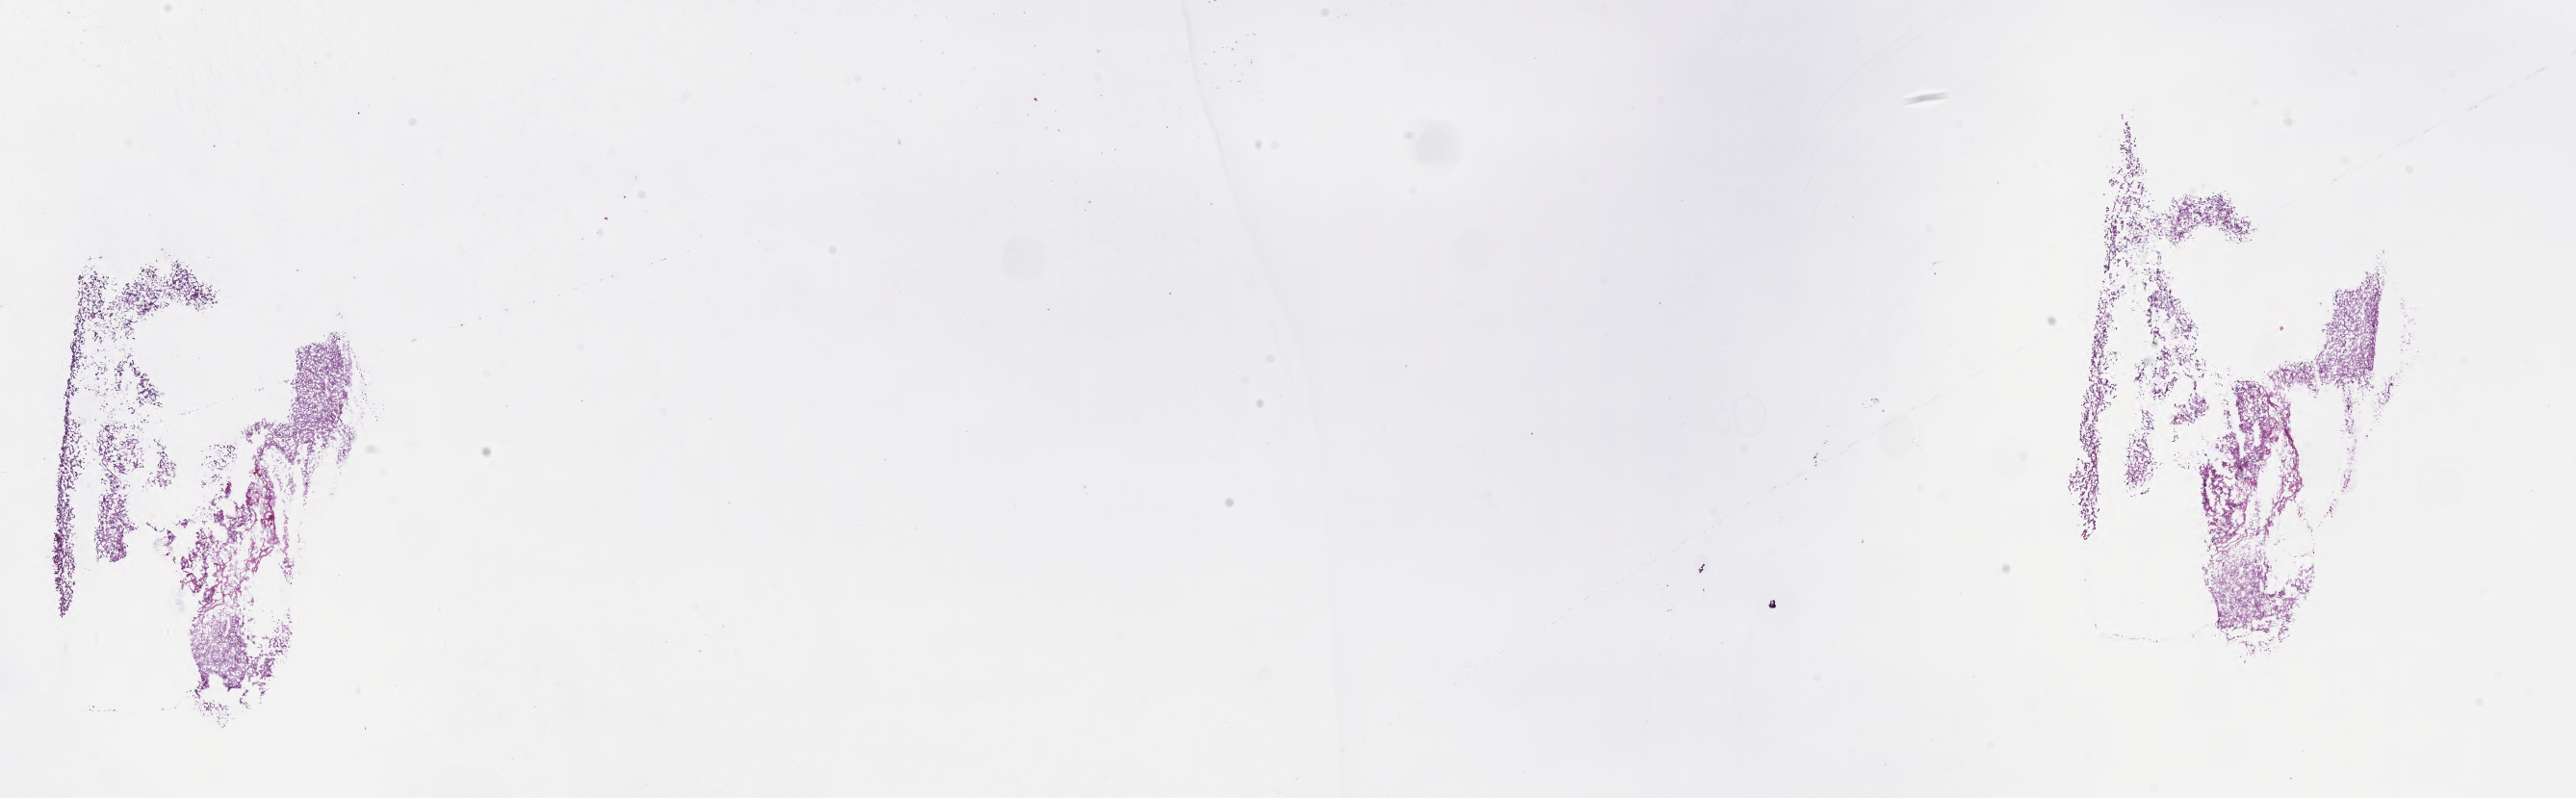
Whole-slide image, haematoxylin and eosin stain of tumor tissue from the brain, whole scanned area (about 21.6 x 6.7 mm) shown as a low-resolution overview. Frozen section. Male patient, age 135 months (11 years 3 months).
Diagnosis (ICD-O-3 morphology term): Pleomorphic xanthoastrocytoma, NOS.